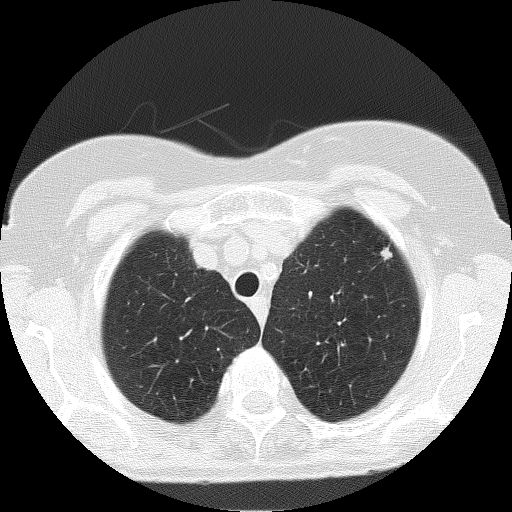
Low-dose screening chest CT, one axial slice; position 142 of 166 along the scan axis; reconstruction kernel FC51; 120 kVp; lung window (W 1500 / L -600 HU); 512 × 512 image matrix, field of view 303 × 303 mm.
Annotated regions visible in this slice (expert manual segmentation):
- lesion 4 (nodule, upper lobe of left lung): bounding box <380,248,392,261> (left, top, right, bottom; pixels)